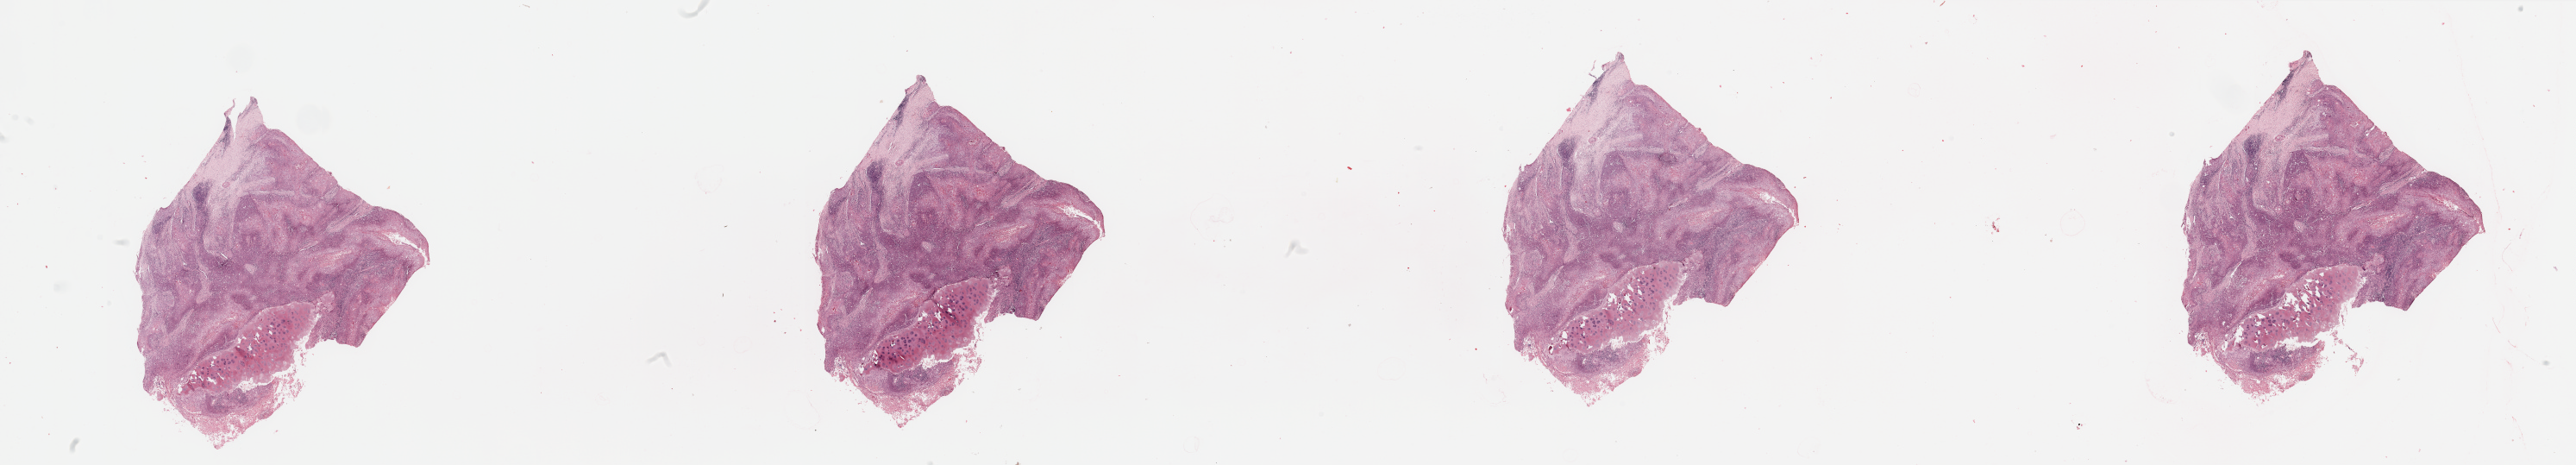
Whole-slide histology image, Hematoxylin and eosin (H&E) stained — low-resolution overview of the scanned area, about 47.3 x 8.5 mm (acquisition: 20x scan). Head and neck, tissue type not recorded. Male, 81 y/o.
- patient diagnosis: Squamous cell carcinoma, NOS (larynx, NOS)